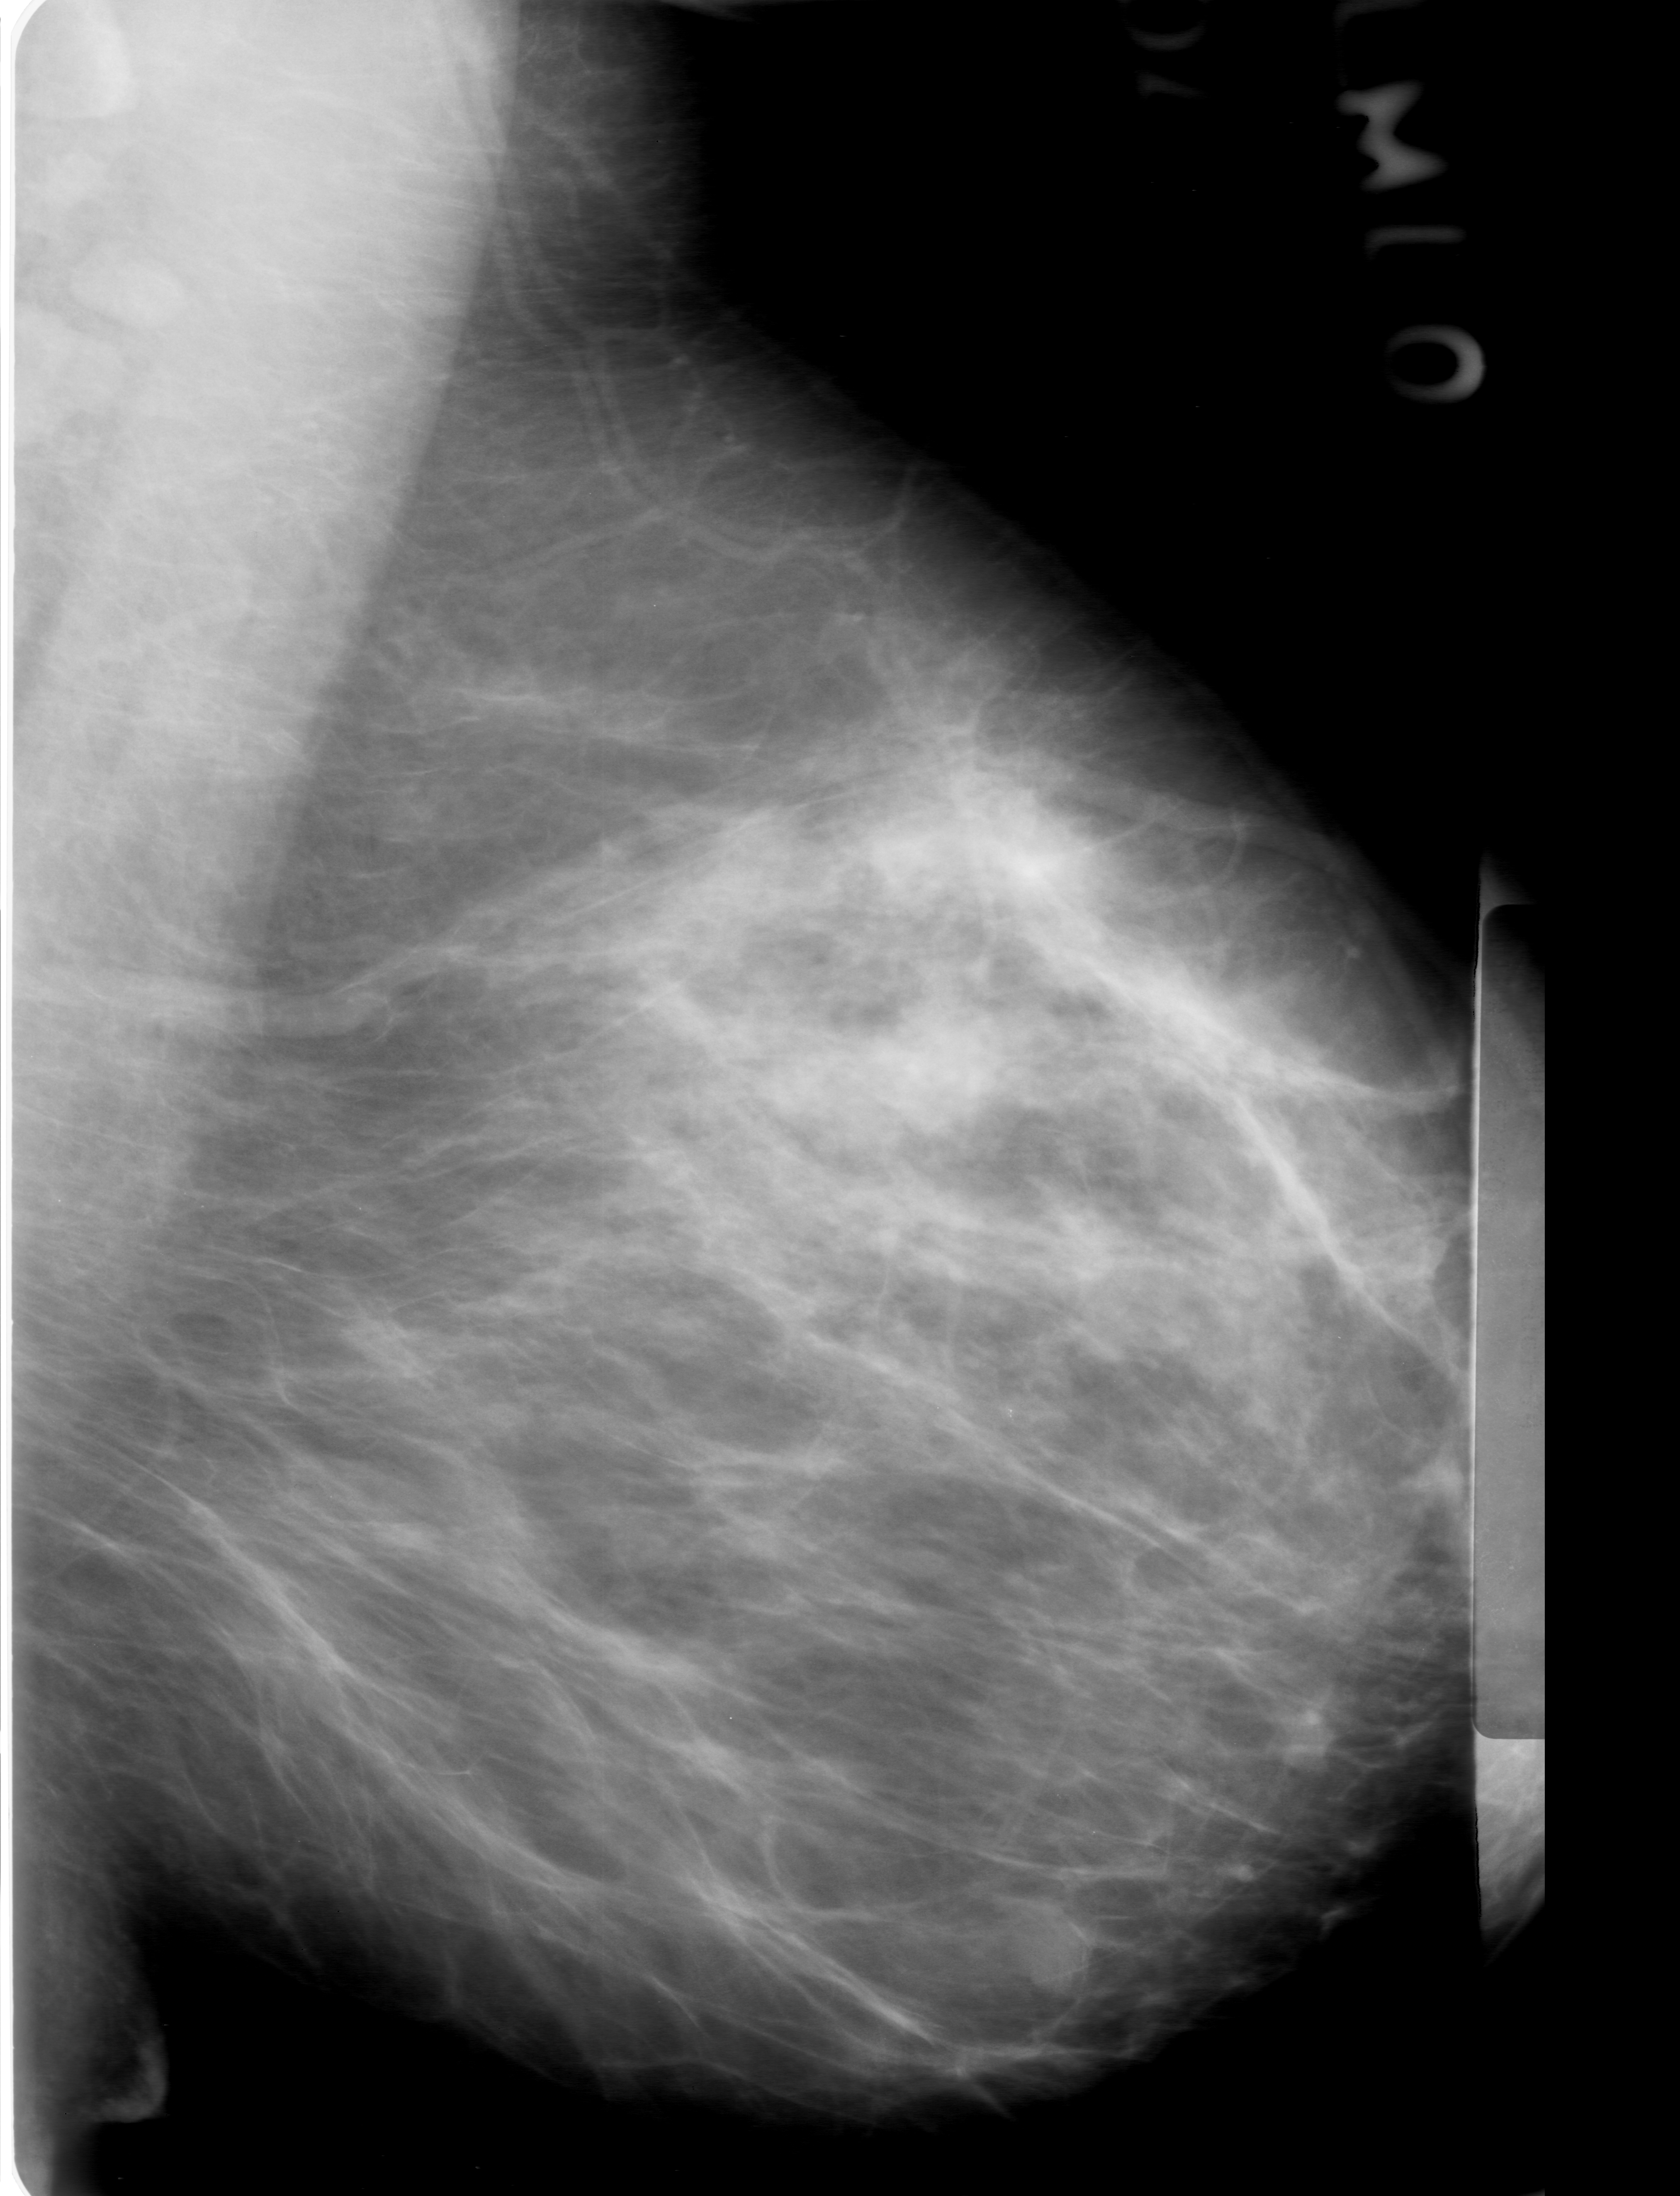
Mammogram (digitized film), left breast, mediolateral oblique (MLO) view.
Mass, shape oval, margins obscured; BI-RADS assessment category 0 (incomplete: needs additional imaging); pathology (as recorded): benign.